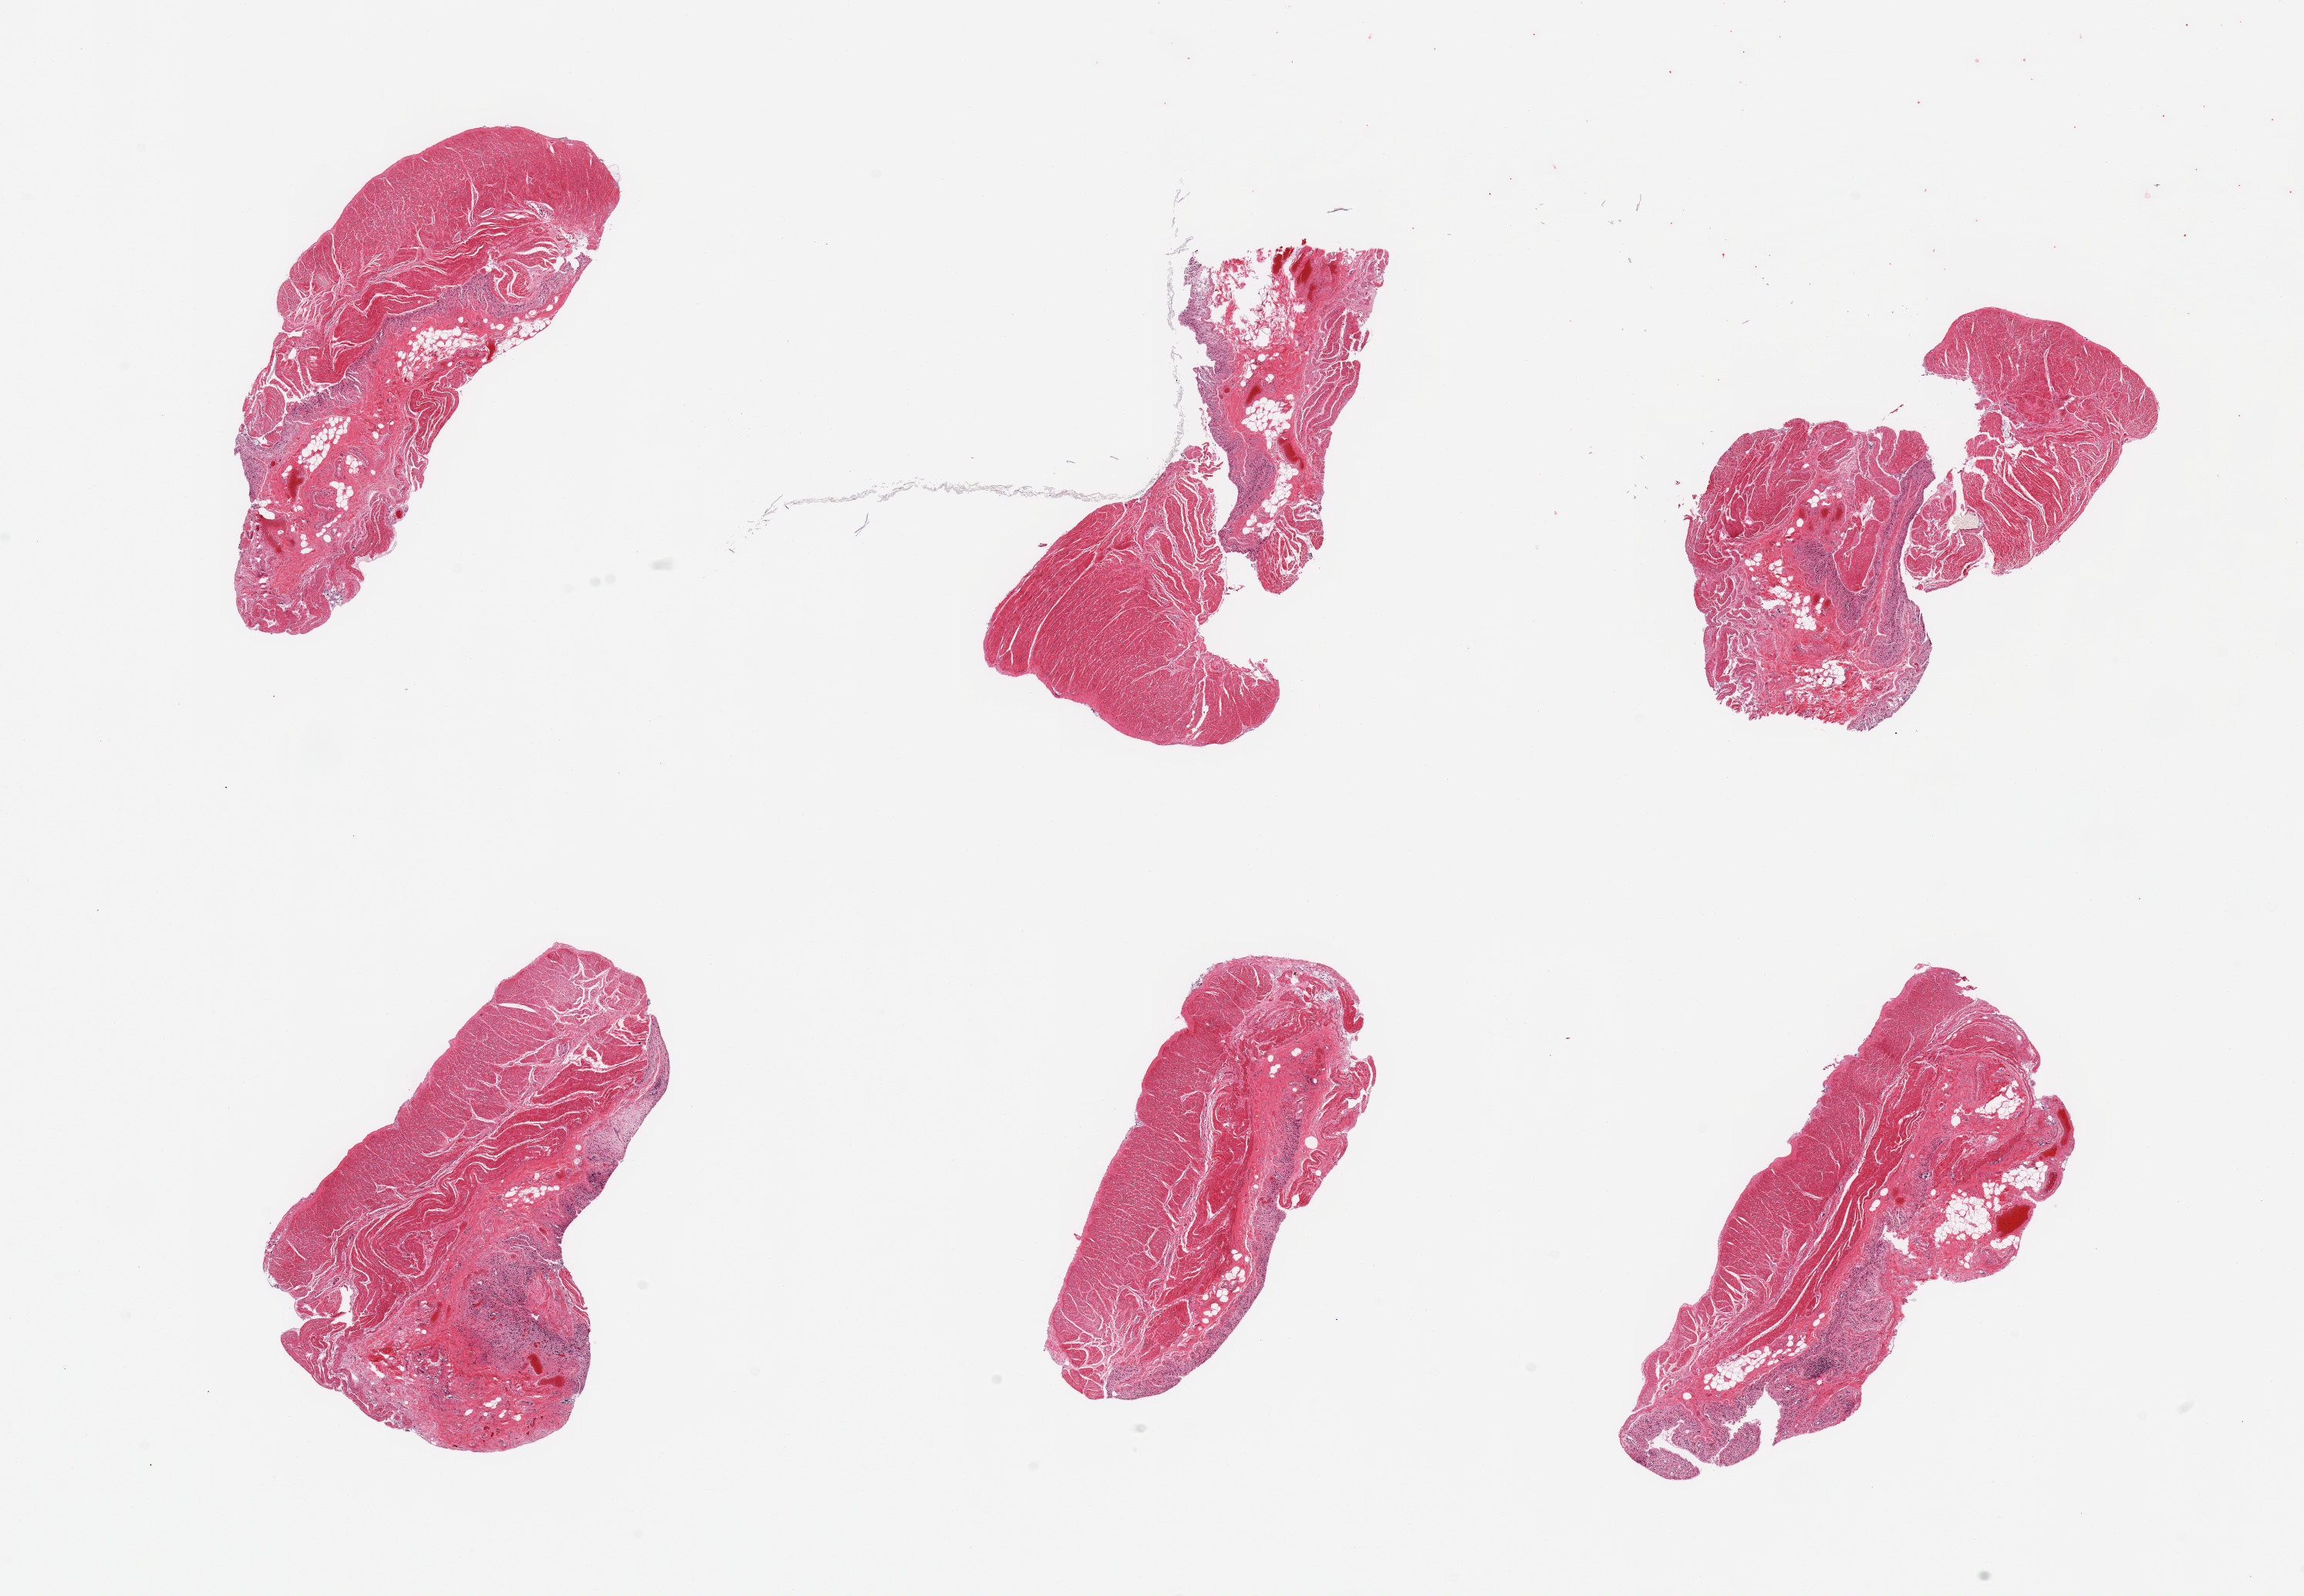
Whole-slide image, hematoxylin and eosin (H&E) stain — a low-resolution overview of the entire scanned area, about 23.6 x 16.4 mm. PAXgene-fixed paraffin-embedded (PFPE) section. Section of transverse colon (target tissue). Donor tissue sample. Donor: male.
Reviewer comment on this tissue sample: 6 pieces; mucosa (3) and muscularis (2).